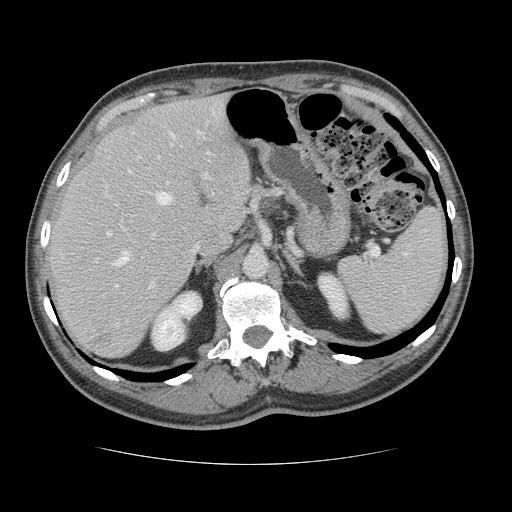
Contrast-enhanced abdominal CT, one axial slice. Slice 88 of 134 in the series (ordered by position). Intravenous contrast given. Soft-tissue window (W 400 / L 40 HU). 2.5 mm slice thickness. 512 × 512 image matrix, field of view 377 × 377 mm. Male patient, age 68 years. From the clinical record (not read from this slice): diagnosis: colorectal cancer liver metastases, imaged before liver resection; multiple liver metastases: yes; largest metastasis: 2.2 cm; disease in both lobes: no.
Outlined on this slice (manually delineated by an expert):
- hepatic veins: box from (x=116, y=133) to (x=213, y=265) px
- liver: (x=48, y=97)–(x=251, y=357)
- planned liver remnant (the part of the liver to remain after resection): (x=48, y=97)–(x=251, y=337)
- portal vein (with intrahepatic branches): (x=107, y=130)–(x=211, y=287)
- liver metastasis: (x=97, y=333)–(x=112, y=346)